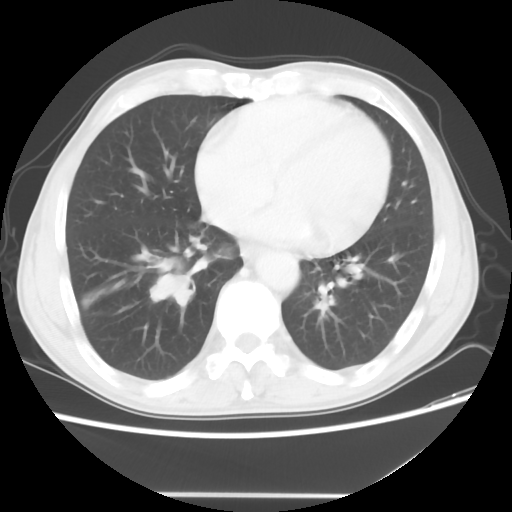
Chest CT, one axial slice; reconstruction kernel STANDARD; 120 kVp; lung window (W 1500 / L -600 HU); 5 mm slice thickness; 512 × 512 image matrix, field of view 344 × 344 mm. Male patient, age 65 years. Case-level facts recorded for this patient, not image findings: clinical TNM (as recorded): T1c N3 M0.
Outlined on this slice (rectangle marked by the reading radiologist):
- lung tumour (recorded histology: small cell carcinoma): bounding box [x1, y1, x2, y2] px = [141, 250, 211, 306]